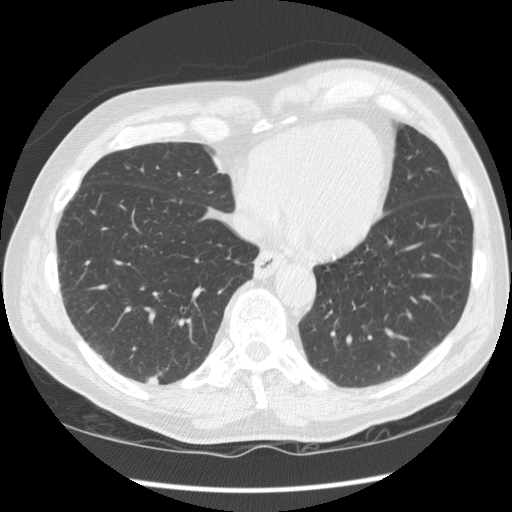
Chest CT (low-dose screening protocol), one axial image, baseline annual screen, lung window (W 1500 / L -600 HU), standard (soft-tissue) reconstruction kernel (STANDARD), 512 × 512 image matrix, field of view 360 × 360 mm. Male, age 71 years at enrolment. Current smoker at enrolment.
• Lesion marked by an expert reader, bounding box (x1, y1, x2, y2) in pixels: (135, 365, 168, 395).
• Reader record for this screening exam (exam-level; its link to the box is not recorded): non-calcified nodule or mass ≥4 mm, right upper lobe, 26 × 15 mm, smooth margins, mixed attenuation.
• Official screen result: positive, change unspecified: nodule(s) >= 4 mm or enlarging nodule(s), mass(es), or other non-specific abnormalities suspicious for lung cancer.
• Lung cancer was diagnosed 357 days after this screen (after the second annual screen): squamous cell carcinoma, NOS, right lower lobe, moderately differentiated (G2), stage IA (AJCC 6th edition), 27 mm at pathology.